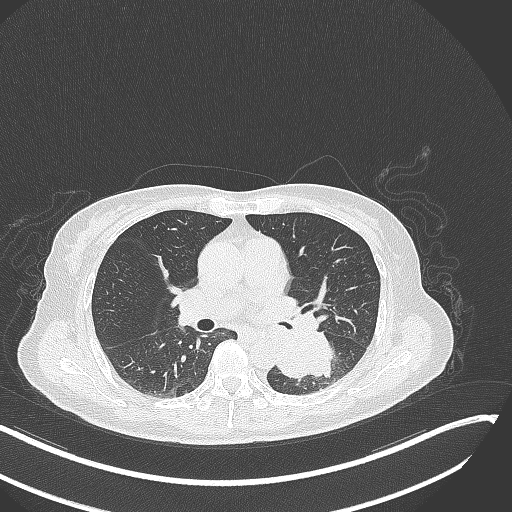
Chest CT, one axial slice. Slice 152 of 342 in the series (ordered by position). Reconstruction kernel B70f. Lung window (W 1500 / L -600 HU). 1 mm slice thickness. 512 × 512 image matrix, field of view 400 × 400 mm. Female patient, age 64 years. From the clinical record (not read from this slice): clinical TNM (as recorded): T3 N1 M1.
Outlined on this slice (bounding box drawn by a radiologist):
- lung tumour (recorded histology: small cell carcinoma): bounding box (x1, y1, x2, y2) in pixels: (274, 329, 339, 386)